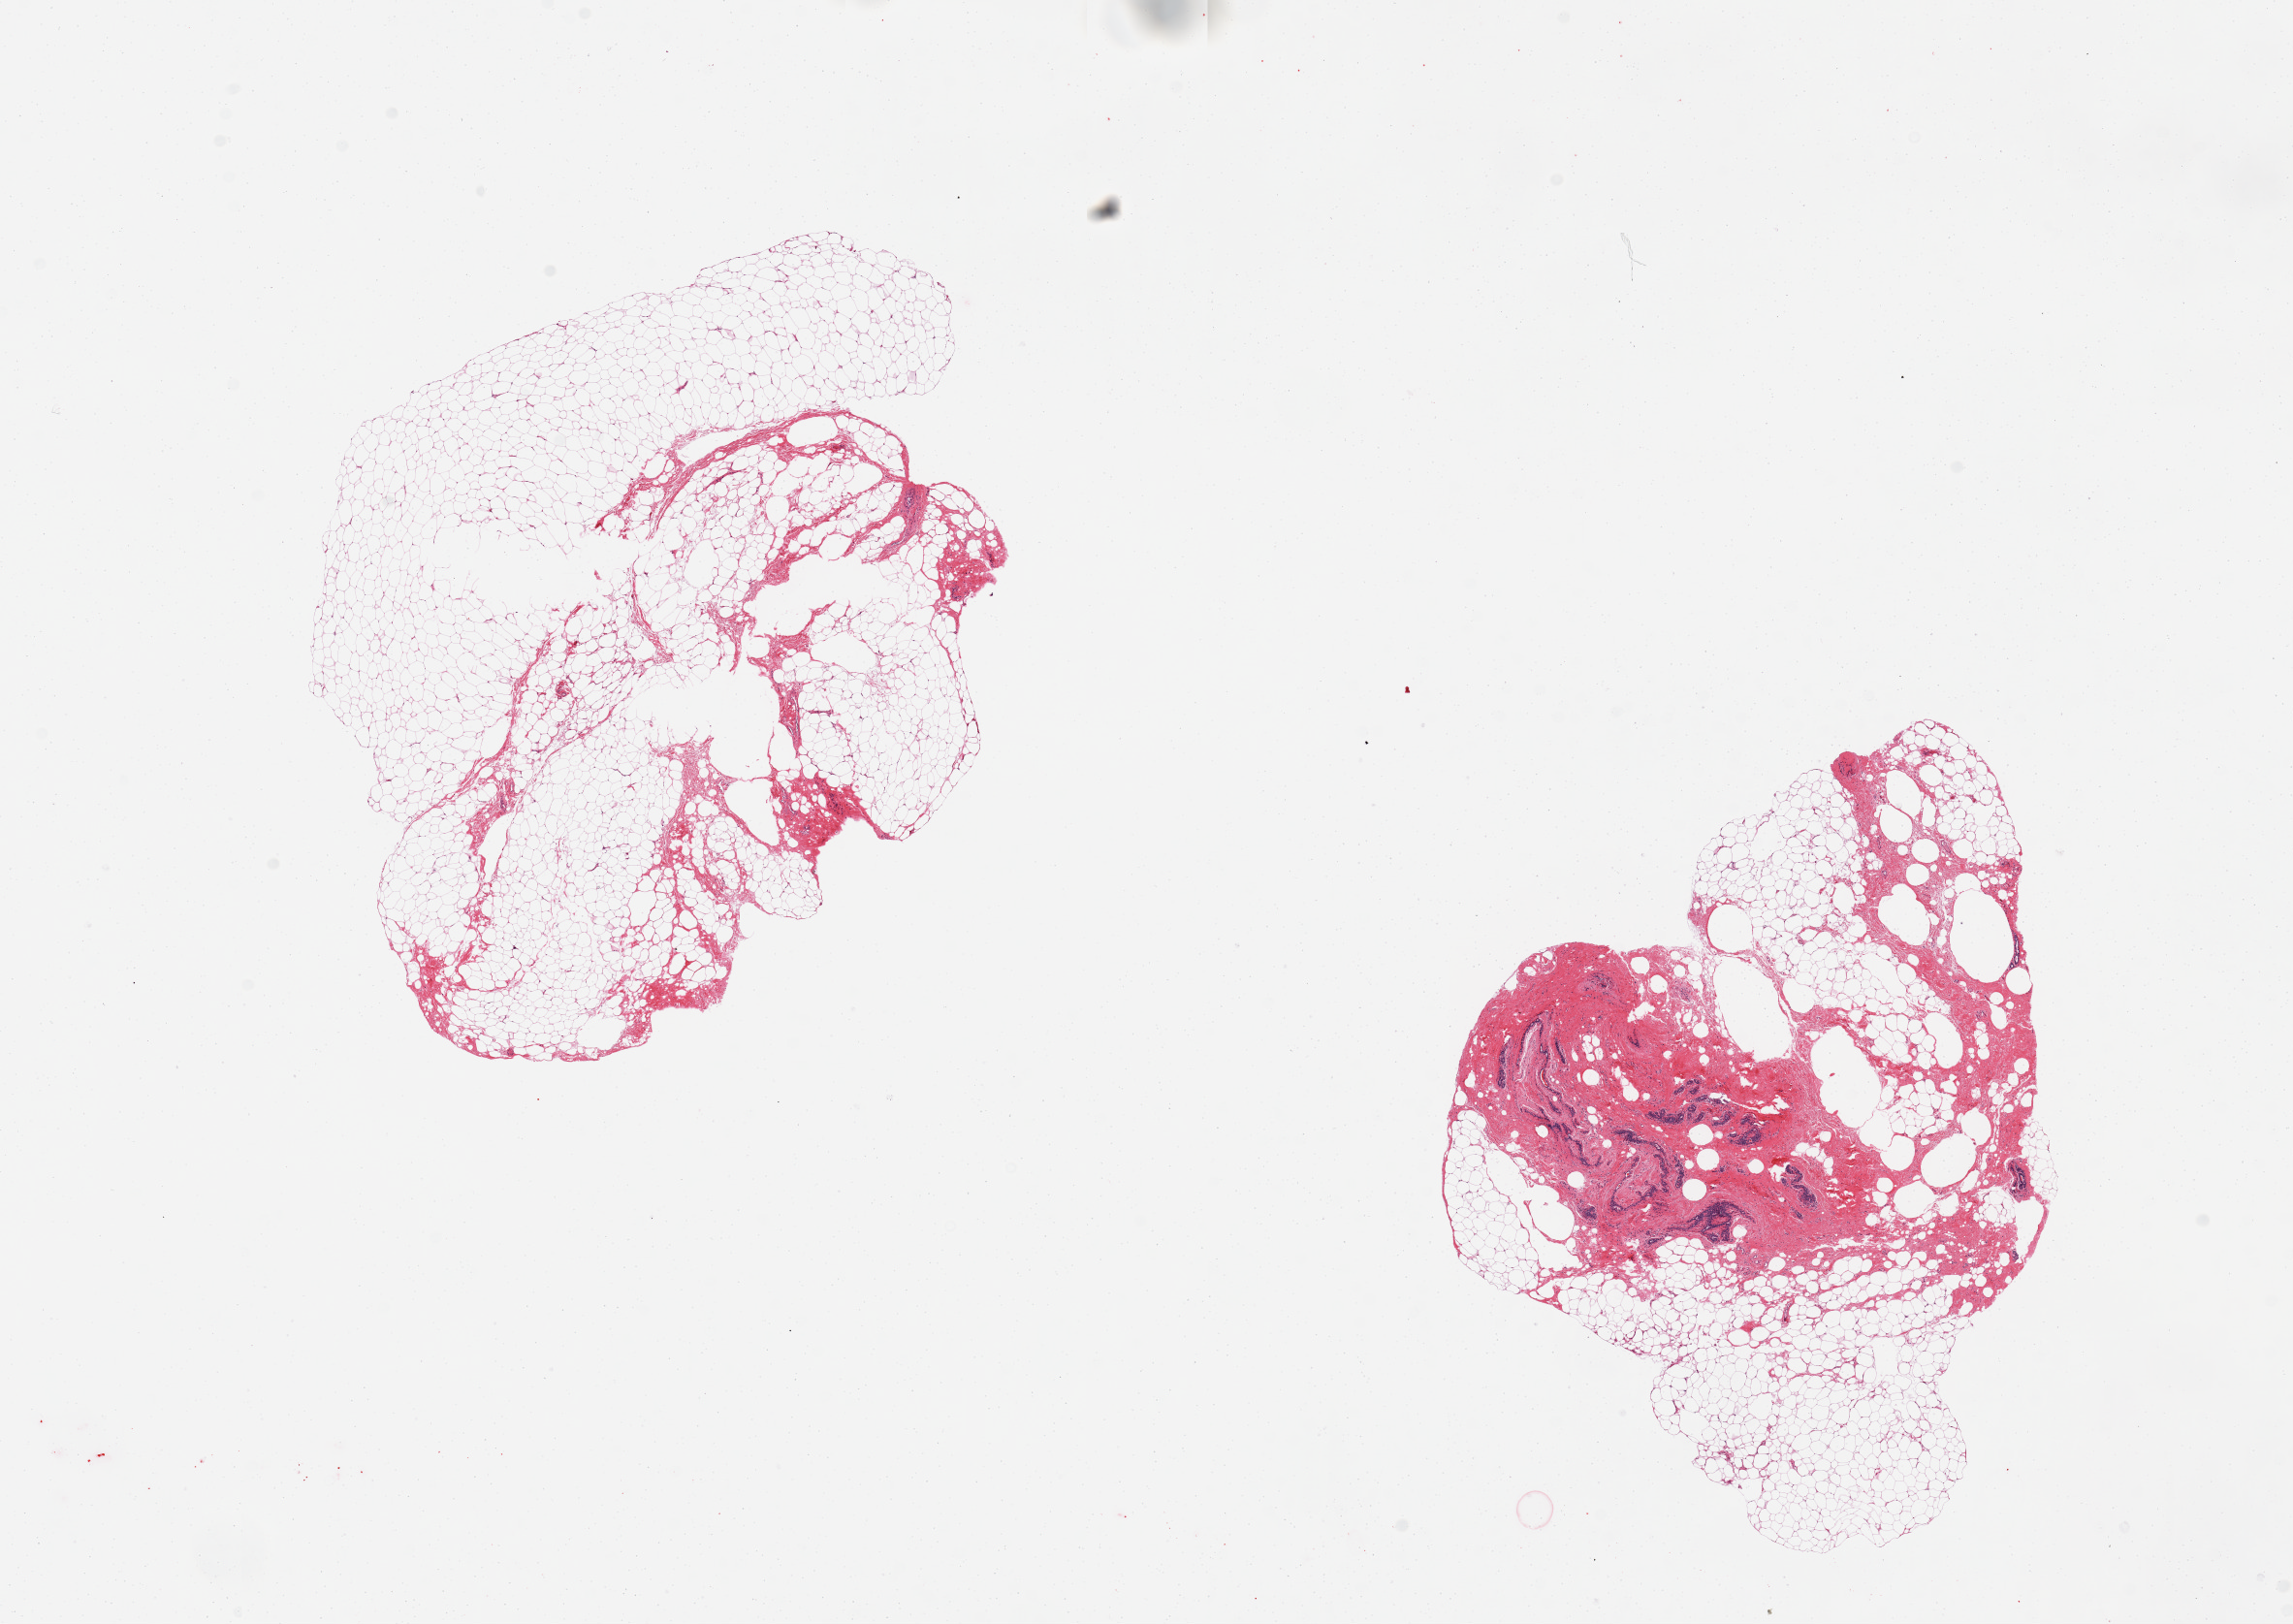
Digitized haematoxylin and eosin-stained section — a low-resolution overview of the entire scanned area, about 18.7 x 13.2 mm (acquisition: 20x scan); PAXgene-fixed paraffin-embedded (PFPE) section; sampled site (target tissue): breast; donor tissue sample. Donor: female.
• pathologist's review note for this sample: 2 pieces, one piece is predominantly fatty, second is 50% fat/50% fibrous stroma and ductal elements